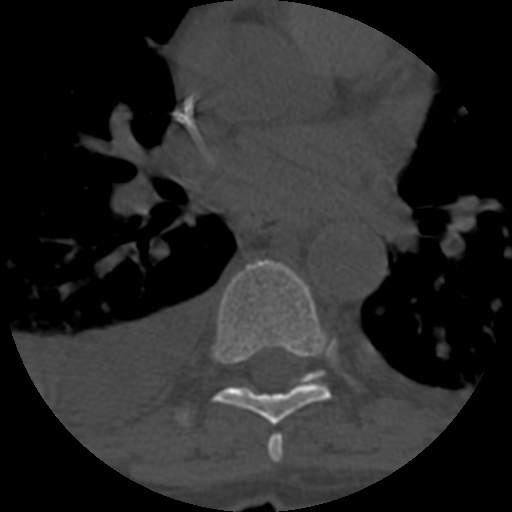
CT including the spine, one axial slice. Position 414 of 708 along the scan axis. Reconstruction kernel STANDARD. 120 kVp. One of 3 acquisitions stored at this slice position. Bone window (W 1800 / L 400 HU). 1.25 mm slice thickness. 512 × 512 image matrix, field of view 160 × 160 mm. Patient age 55 years. Case-level facts recorded for this patient, not image findings: primary cancer: colon; vertebrae with lytic lesions (as recorded): T12, L1, L5.
Structures marked on this image (semi-automatic segmentation, software-assisted and operator-edited):
- T6 vertebra: bounding box <267,434,284,463> (left, top, right, bottom; pixels)
- T7 vertebra: <211,259,330,425>
- T8 vertebra: <303,370,324,382>